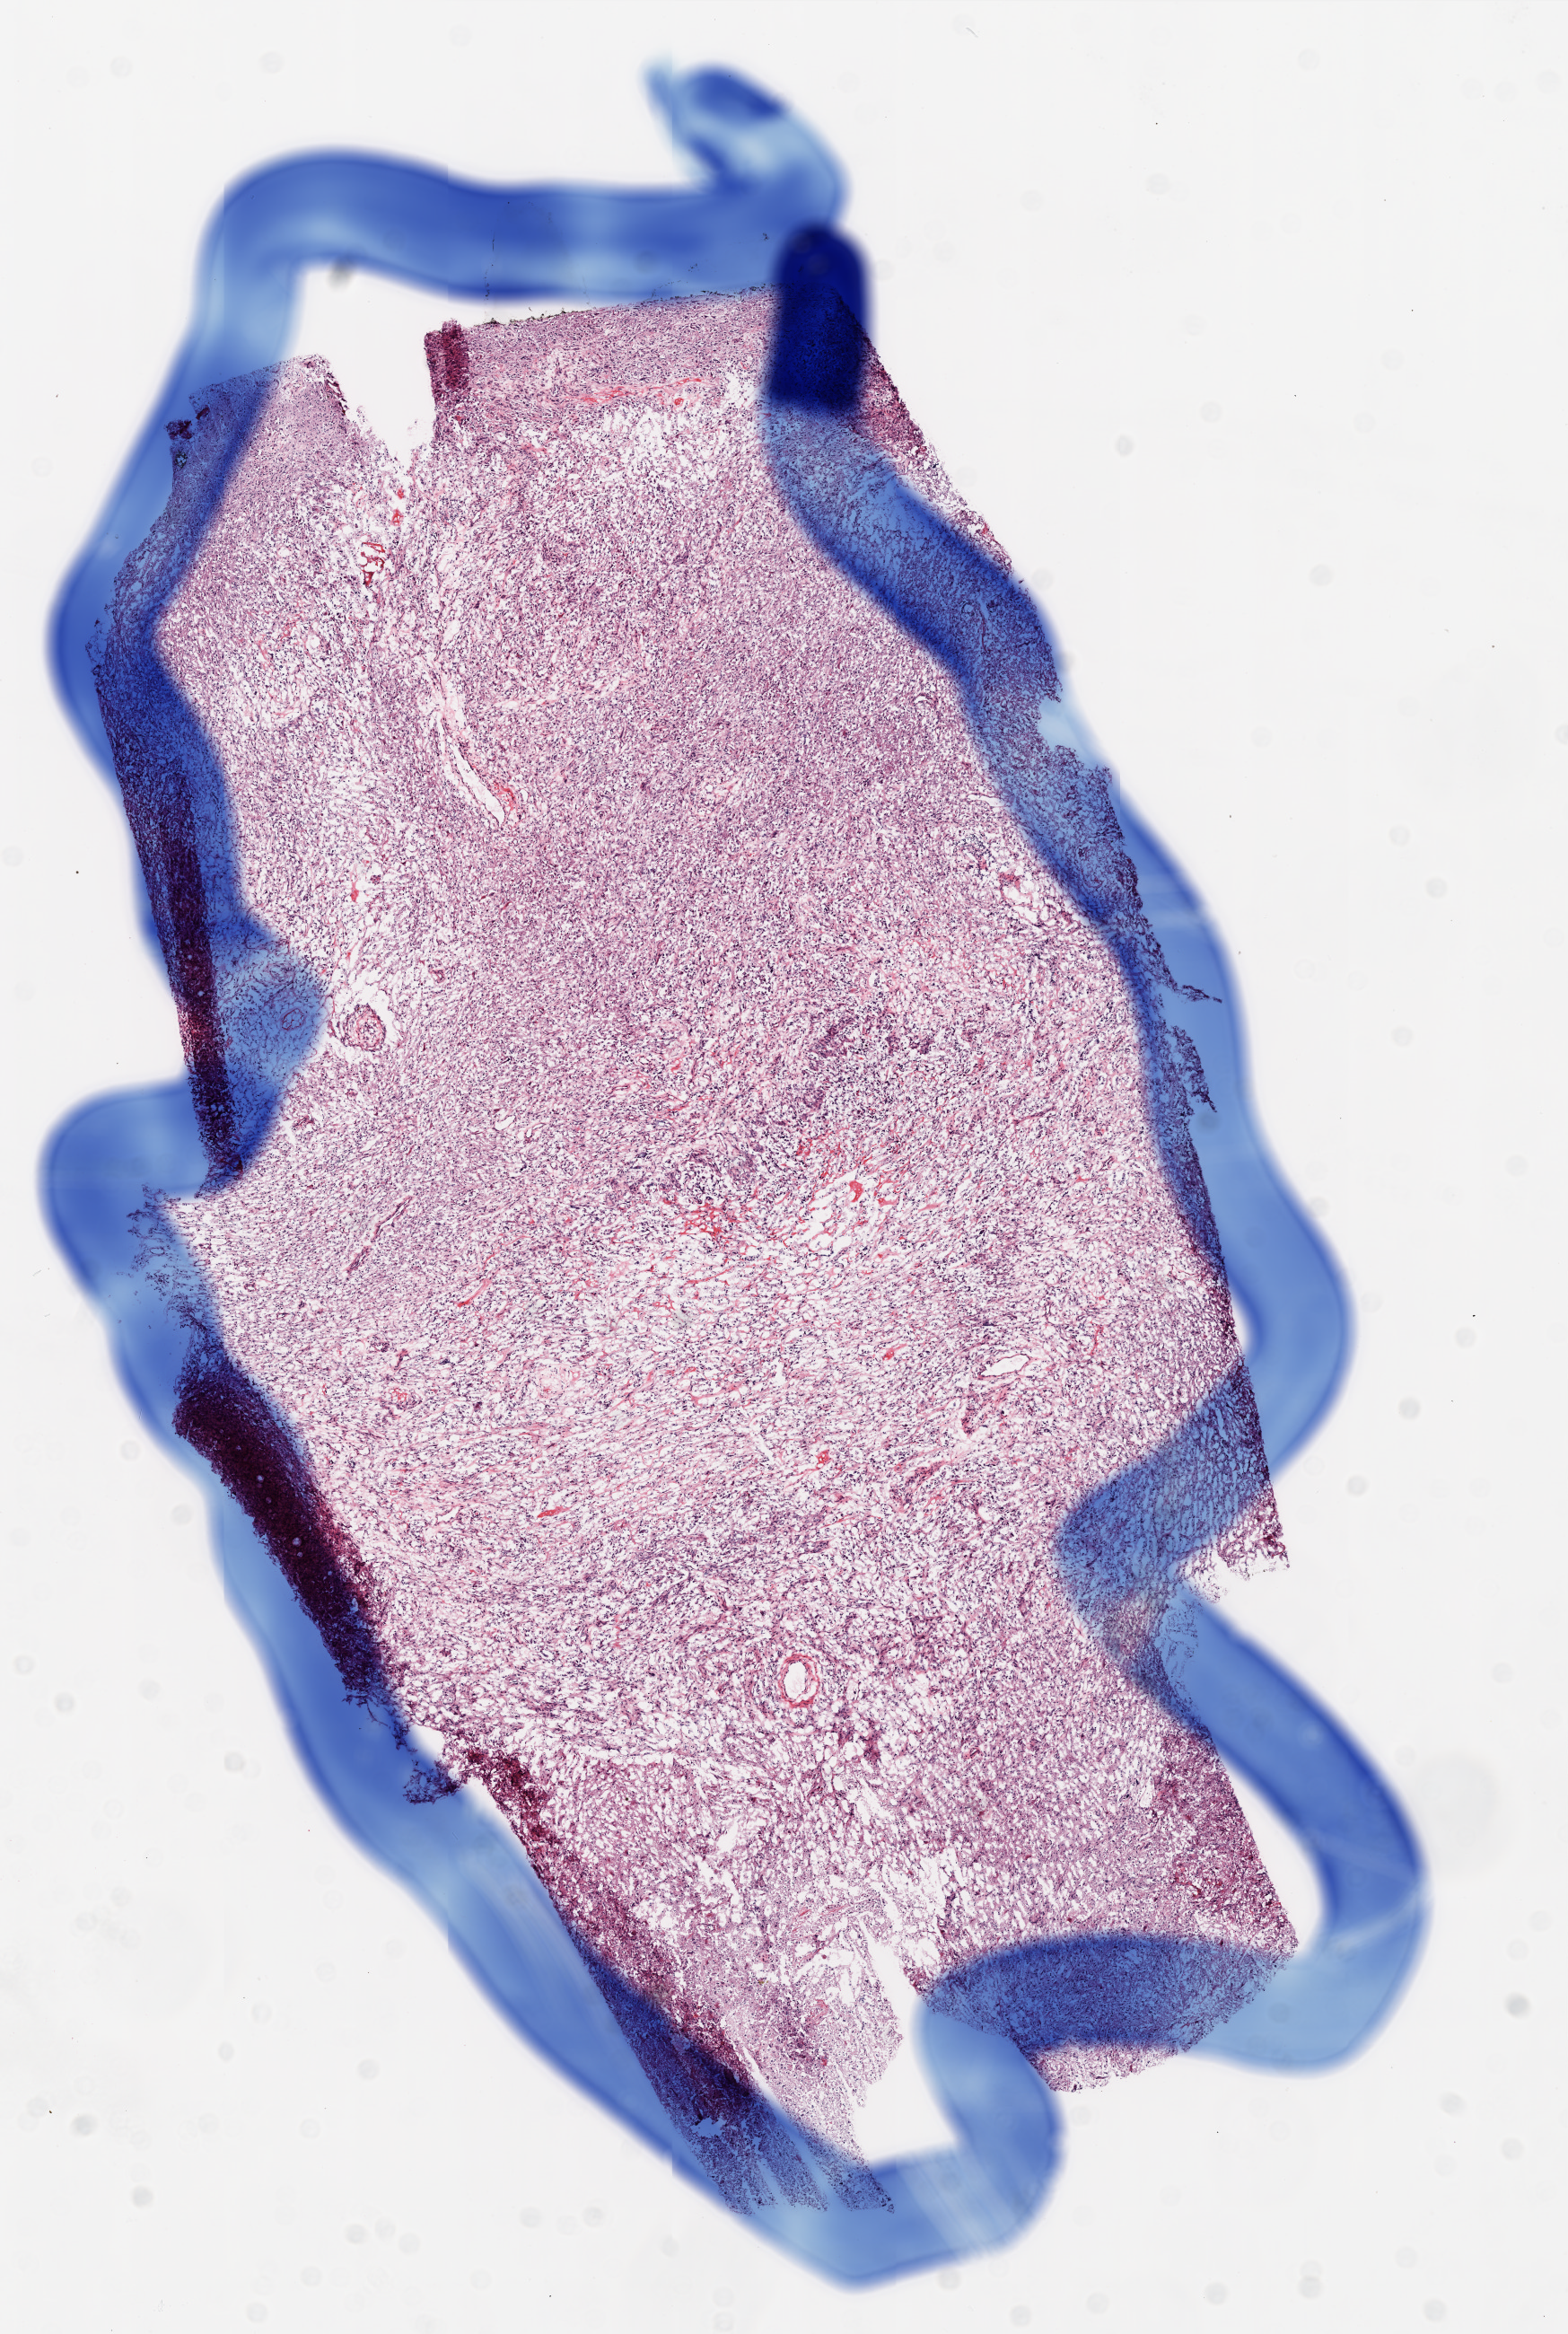
Digitized Hematoxylin and eosin (H&E) stained tissue section (whole slide), a low-resolution overview of the entire scanned area, about 7.0 x 10.4 mm (acquisition: 20x scan), frozen section from the top of the tissue portion, primary tumour sample from the brain. Patient: female, age at initial diagnosis 51 years.
Pathologic diagnosis: Glioblastoma.